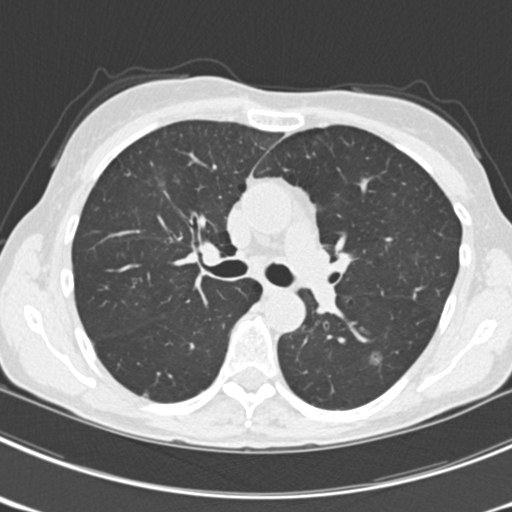
Axial slice from a low-dose chest CT screening exam; third screening round (two years after baseline); lung window (W 1500 / L -600 HU); 2 mm slice thickness; 120 kVp; slice 79 of 225 in the series; 512 × 512 image matrix. Female participant, aged 63 years at enrolment.
• Lesion marked by an expert reader, bounding box <358,340,397,380> (left, top, right, bottom; pixels).
• The screening reader recorded 9 non-calcified nodules or masses ≥4 mm on this exam (left upper lobe, right upper lobe, left upper lobe, left lower lobe, right middle lobe, left lower lobe, left lower lobe, right lower lobe, right lower lobe); which of them this box marks is not recorded.
• Lung cancer was diagnosed 15 days after this screen: bronchiolo-alveolar adenocarcinoma, NOS, right upper lobe, right middle lobe, right lower lobe, left upper lobe, left lower lobe, moderately differentiated (G2), stage IV (AJCC 6th edition).